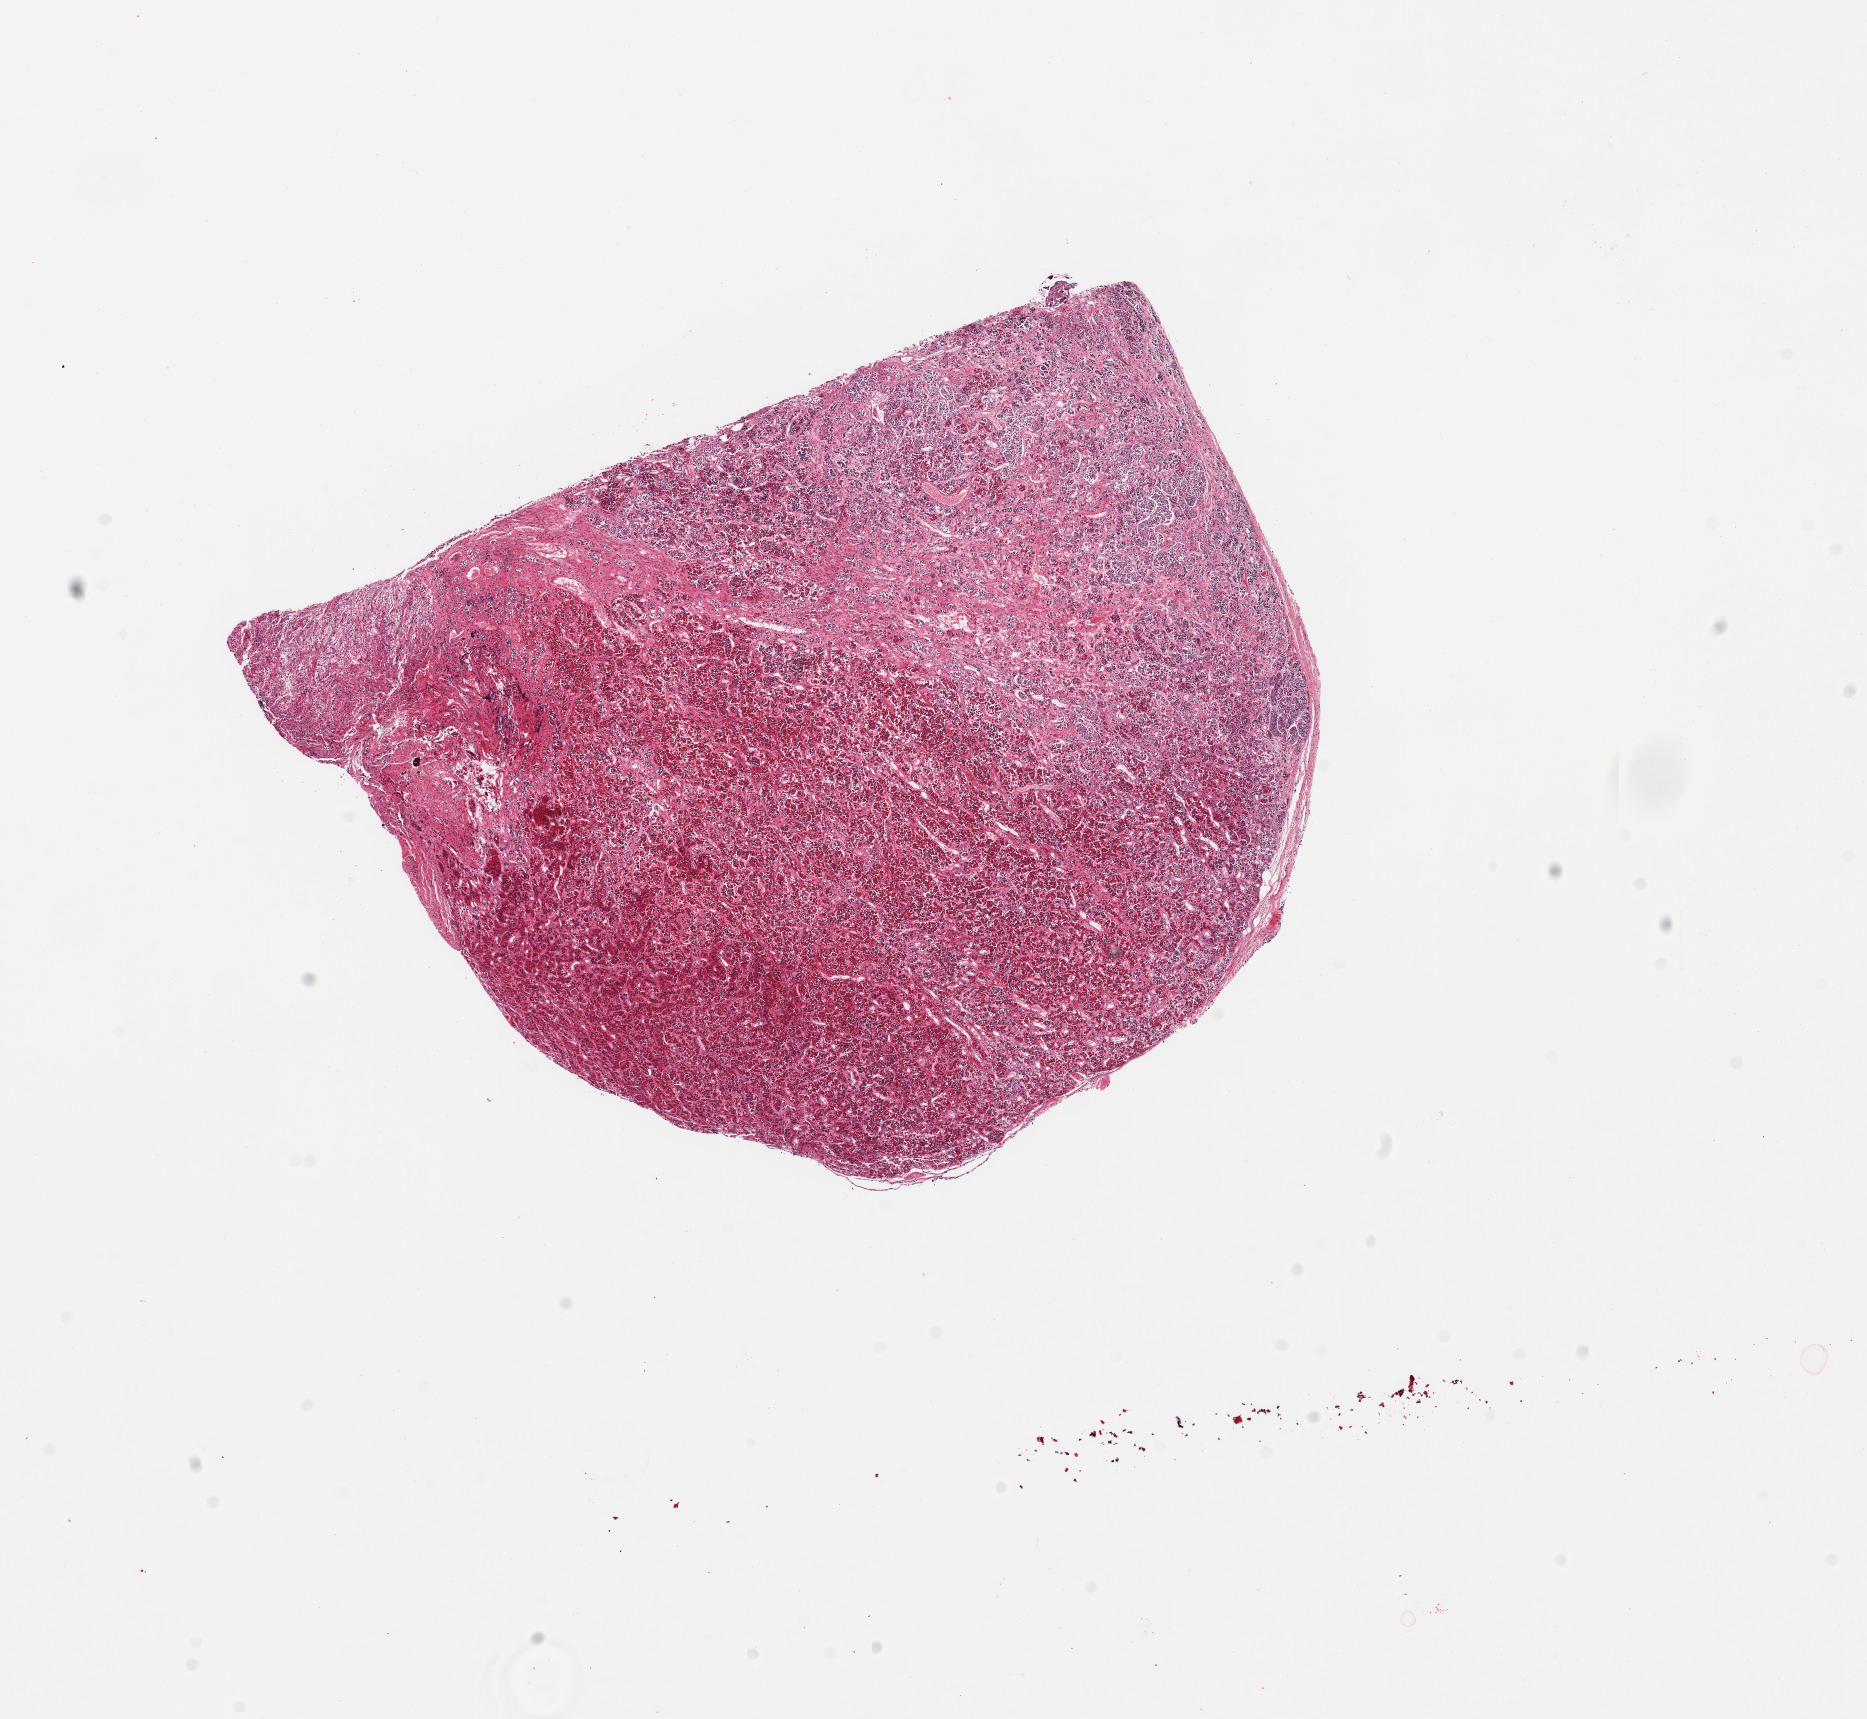
Digitized hematoxylin and eosin (H&E)-stained section, brightfield, a low-resolution overview of the entire scanned area, about 14.8 x 13.6 mm. PAXgene-fixed paraffin-embedded (PFPE) section. Sampled site (target tissue): pituitary. Tissue donor sample. Female donor.
- reviewer comment on this tissue sample: 1 piece, all adenohypophysis. Unusually poorly preserved